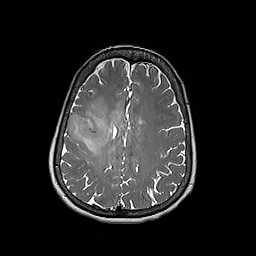
Brain MRI from a brain-tumour surgery series, one axial slice. Slice 74 of 192 in the series (ordered by position). 1 mm slice thickness. 256 × 256 image matrix, field of view 250 × 250 mm. Case-level facts recorded for this patient, not image findings: histopathology: Oligodendroglioma; WHO grade: 3; IDH mutation: yes.
Outlined on this slice (outlined manually by an expert reader):
- tumour: bounding box (x1, y1, x2, y2) in pixels: (67, 113, 109, 150)